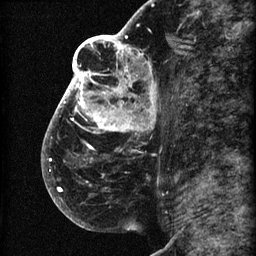
Breast MRI (dynamic contrast-enhanced), one sagittal slice. Position 39 of 60 along the scan axis. 3 images stored at this slice position (order not interpretable as contrast timing). 1.5 T. TE 4.2 ms, TR 22.7 ms. 2 mm slice thickness. 256 × 256 image matrix, field of view 180 × 180 mm. Female patient, age 48 years. Case-level facts recorded for this patient, not image findings: setting: breast cancer imaged before/during neoadjuvant chemotherapy; receptor status: triple-negative.
Structures marked on this image (semi-automatically segmented with operator editing):
- analysis volume of interest (the breast-tissue region the enhancement analysis was run in; not a lesion): box from (x=44, y=30) to (x=173, y=207) px
- tumour enhancement mask (voxels above the 90 % enhancement threshold inside the analysis volume of interest): (x=44, y=30)–(x=154, y=191)